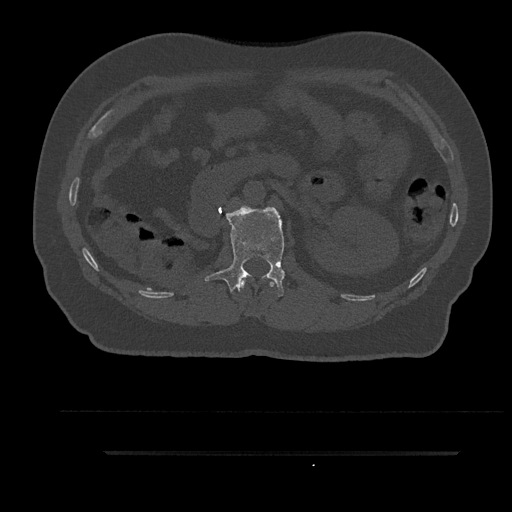
CT including the spine, one axial slice; position 182 of 797 along the scan axis; reconstruction kernel Br40s/3; bone window (W 1800 / L 400 HU); 0.5 mm slice thickness; 512 × 512 image matrix, field of view 432 × 432 mm. Patient: male, 63 years. Case-level facts recorded for this patient, not image findings: primary cancer: renal.
Outlined on this slice (semi-automatically segmented with operator editing):
- L1 vertebra: box from (x=205, y=207) to (x=285, y=297) px
- T12 vertebra: (x=240, y=279)–(x=275, y=289)